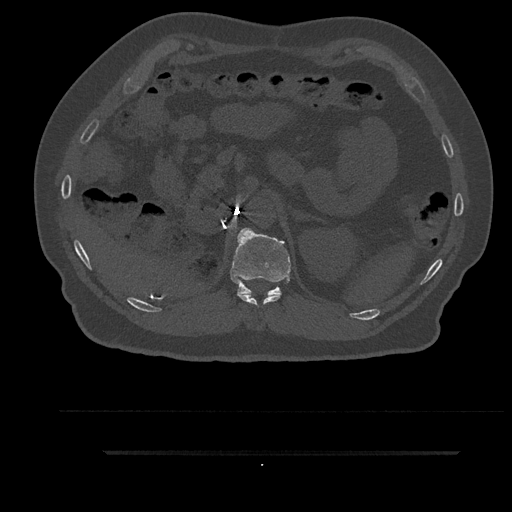
CT including the spine, one axial slice; slice 268 of 797 in the series (ordered by position); reconstruction kernel Br40s/3; bone window (W 1800 / L 400 HU); 0.5 mm slice thickness; 512 × 512 image matrix. Patient: male, 63 years. From the clinical record (not read from this slice): primary cancer: renal.
Outlined on this slice (semi-automatic segmentation, software-assisted and operator-edited):
- T11 vertebra: box from (x=238, y=293) to (x=281, y=307) px
- T12 vertebra: (x=231, y=228)–(x=291, y=296)